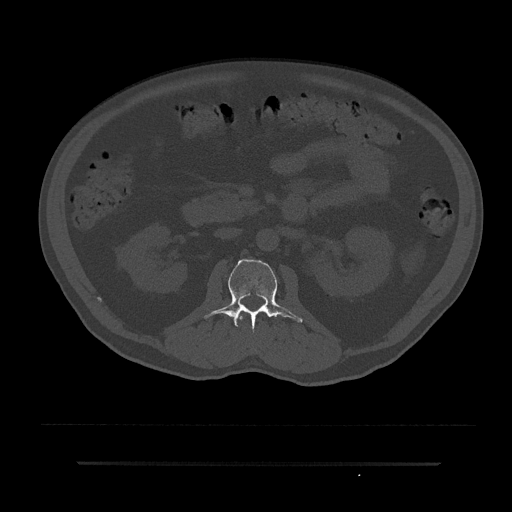
CT including the spine, one axial slice; slice 81 of 797 in the series (ordered by position); bone window (W 1800 / L 400 HU); 512 × 512 image matrix. Male patient, age 59 years. Case-level facts recorded for this patient, not image findings: primary cancer: bile ducts; vertebrae with lytic lesions (as recorded): T10.
Structures marked on this image (semi-automatic segmentation, software-assisted and operator-edited):
- L1 vertebra: box from (x=235, y=311) to (x=244, y=326) px
- L2 vertebra: (x=203, y=259)–(x=303, y=328)